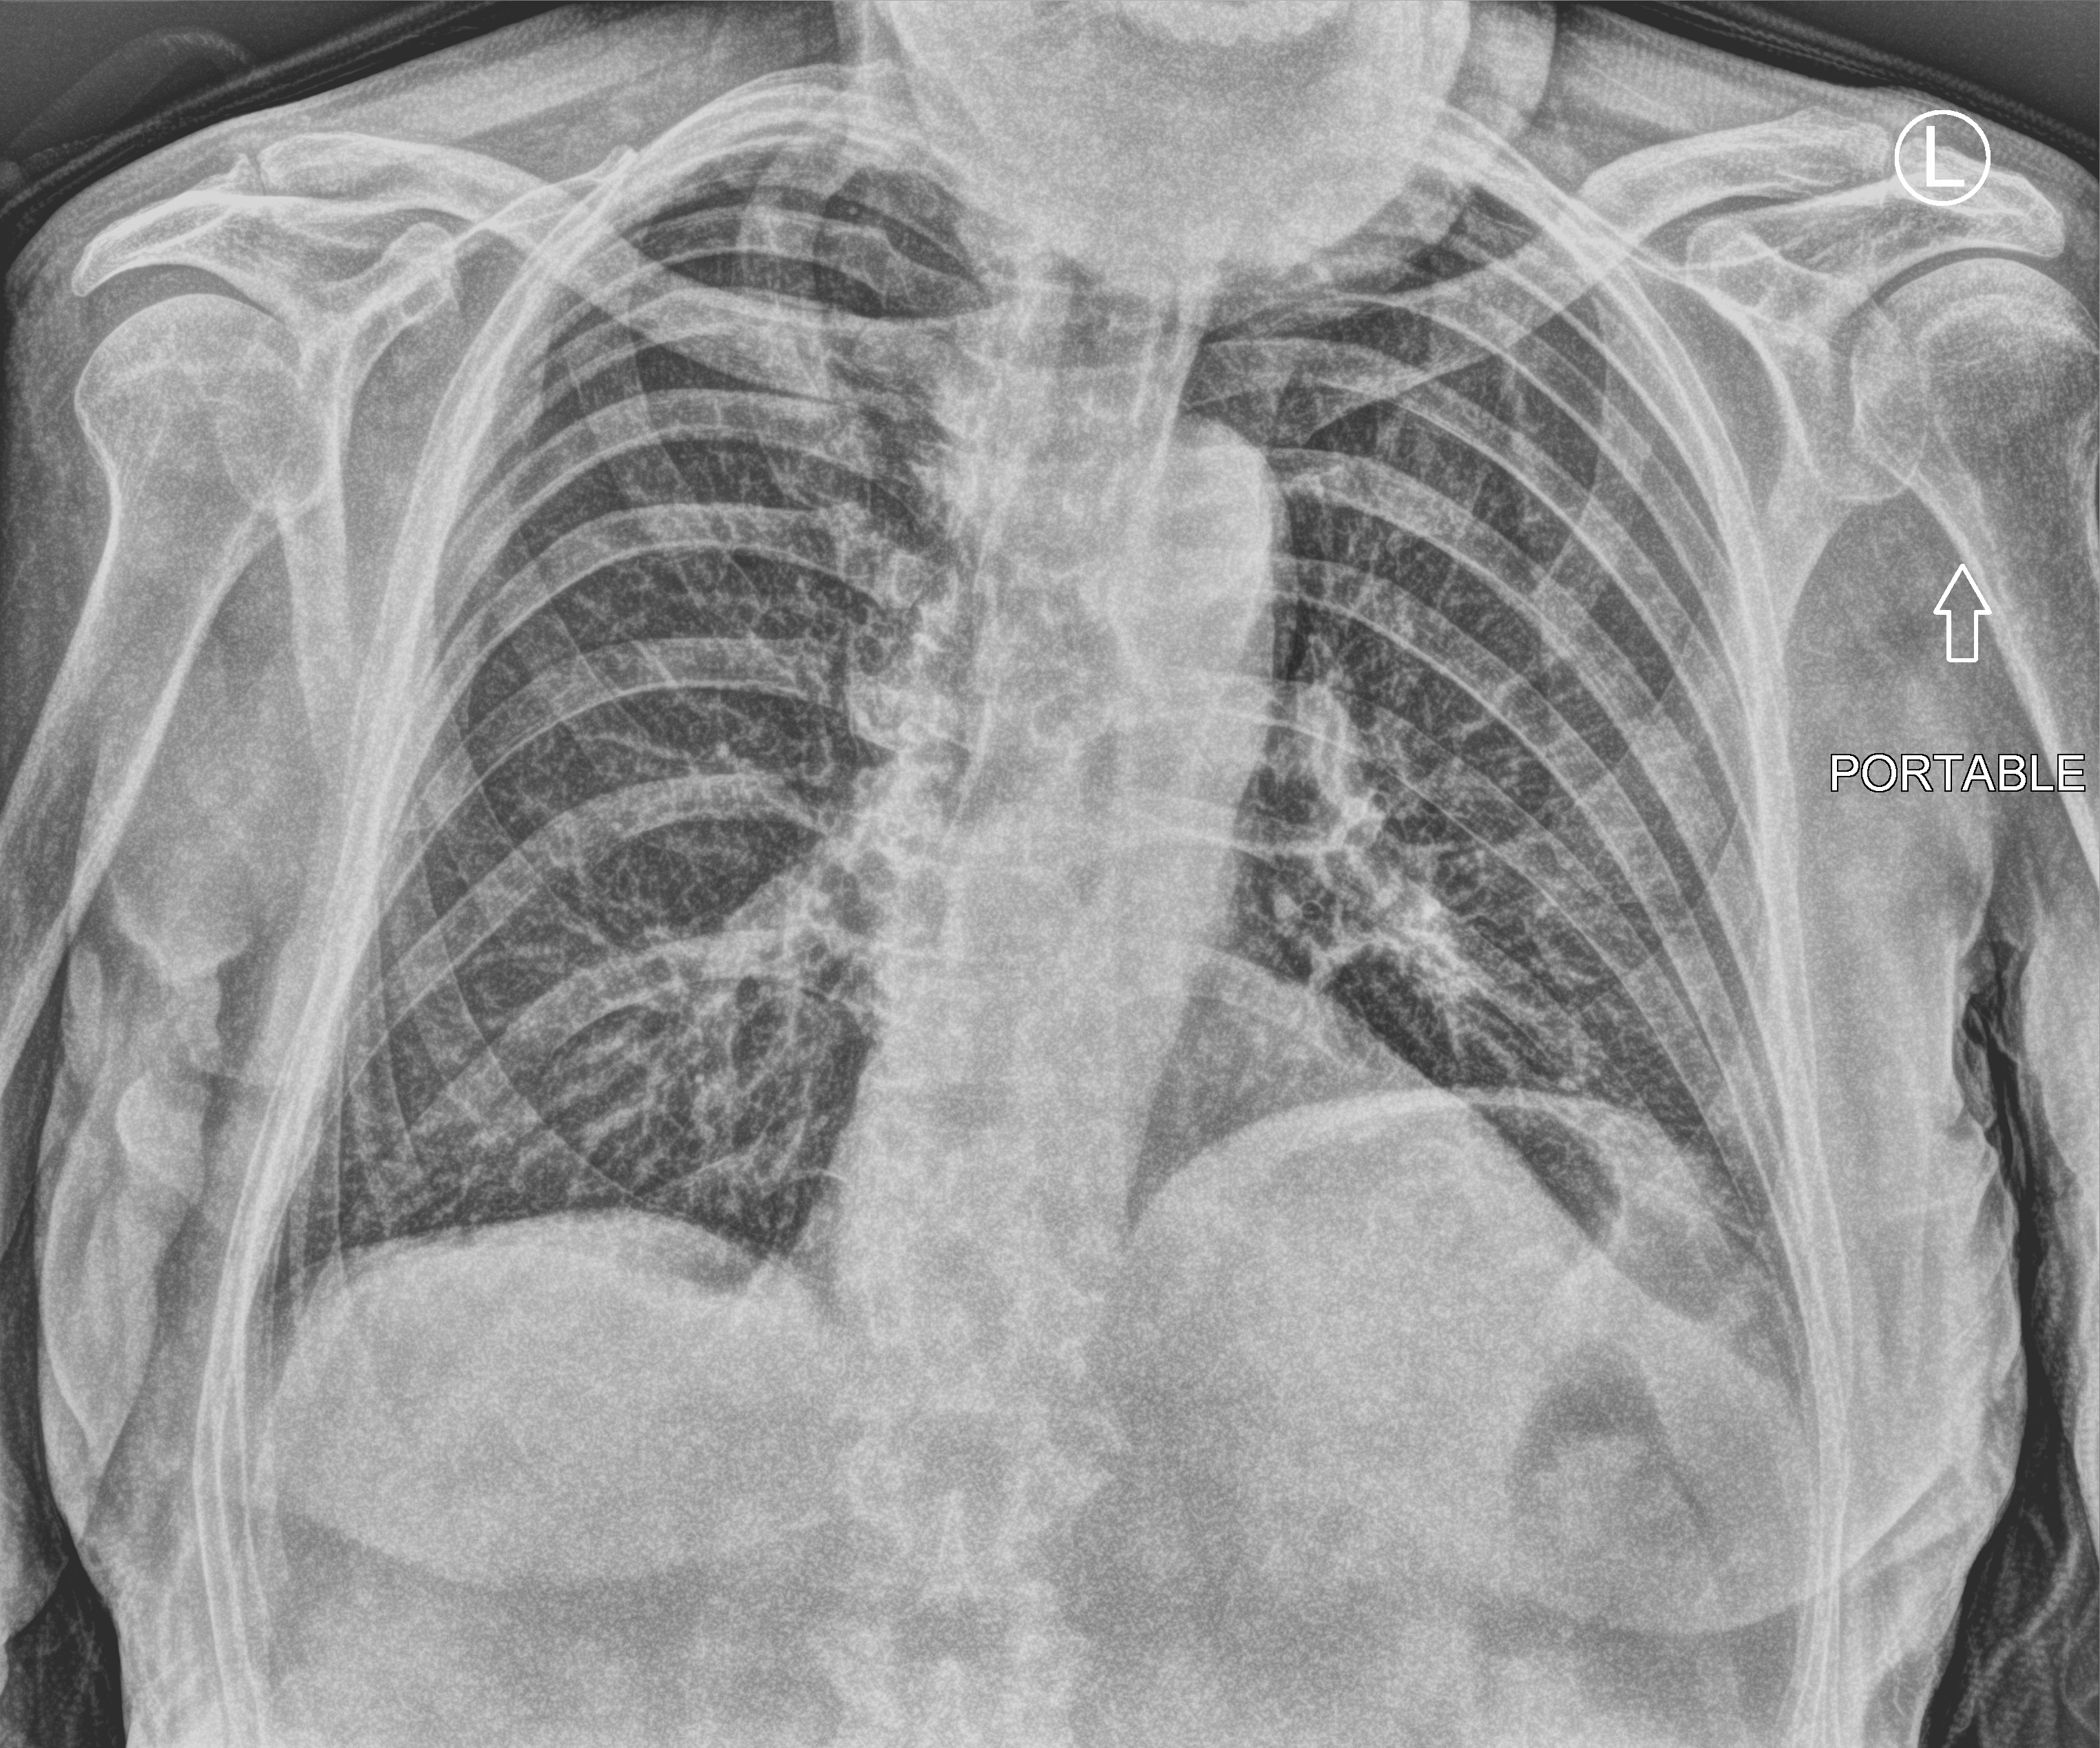
Portable chest radiograph; anteroposterior (AP) projection. Male patient hospitalised with COVID-19, age 75–90 years.
Hospital-stay facts (about this admission, not read from this image; timing relative to this image not recorded):
- admitted to intensive care during this hospital stay: no
- mechanically ventilated during this hospital stay: no